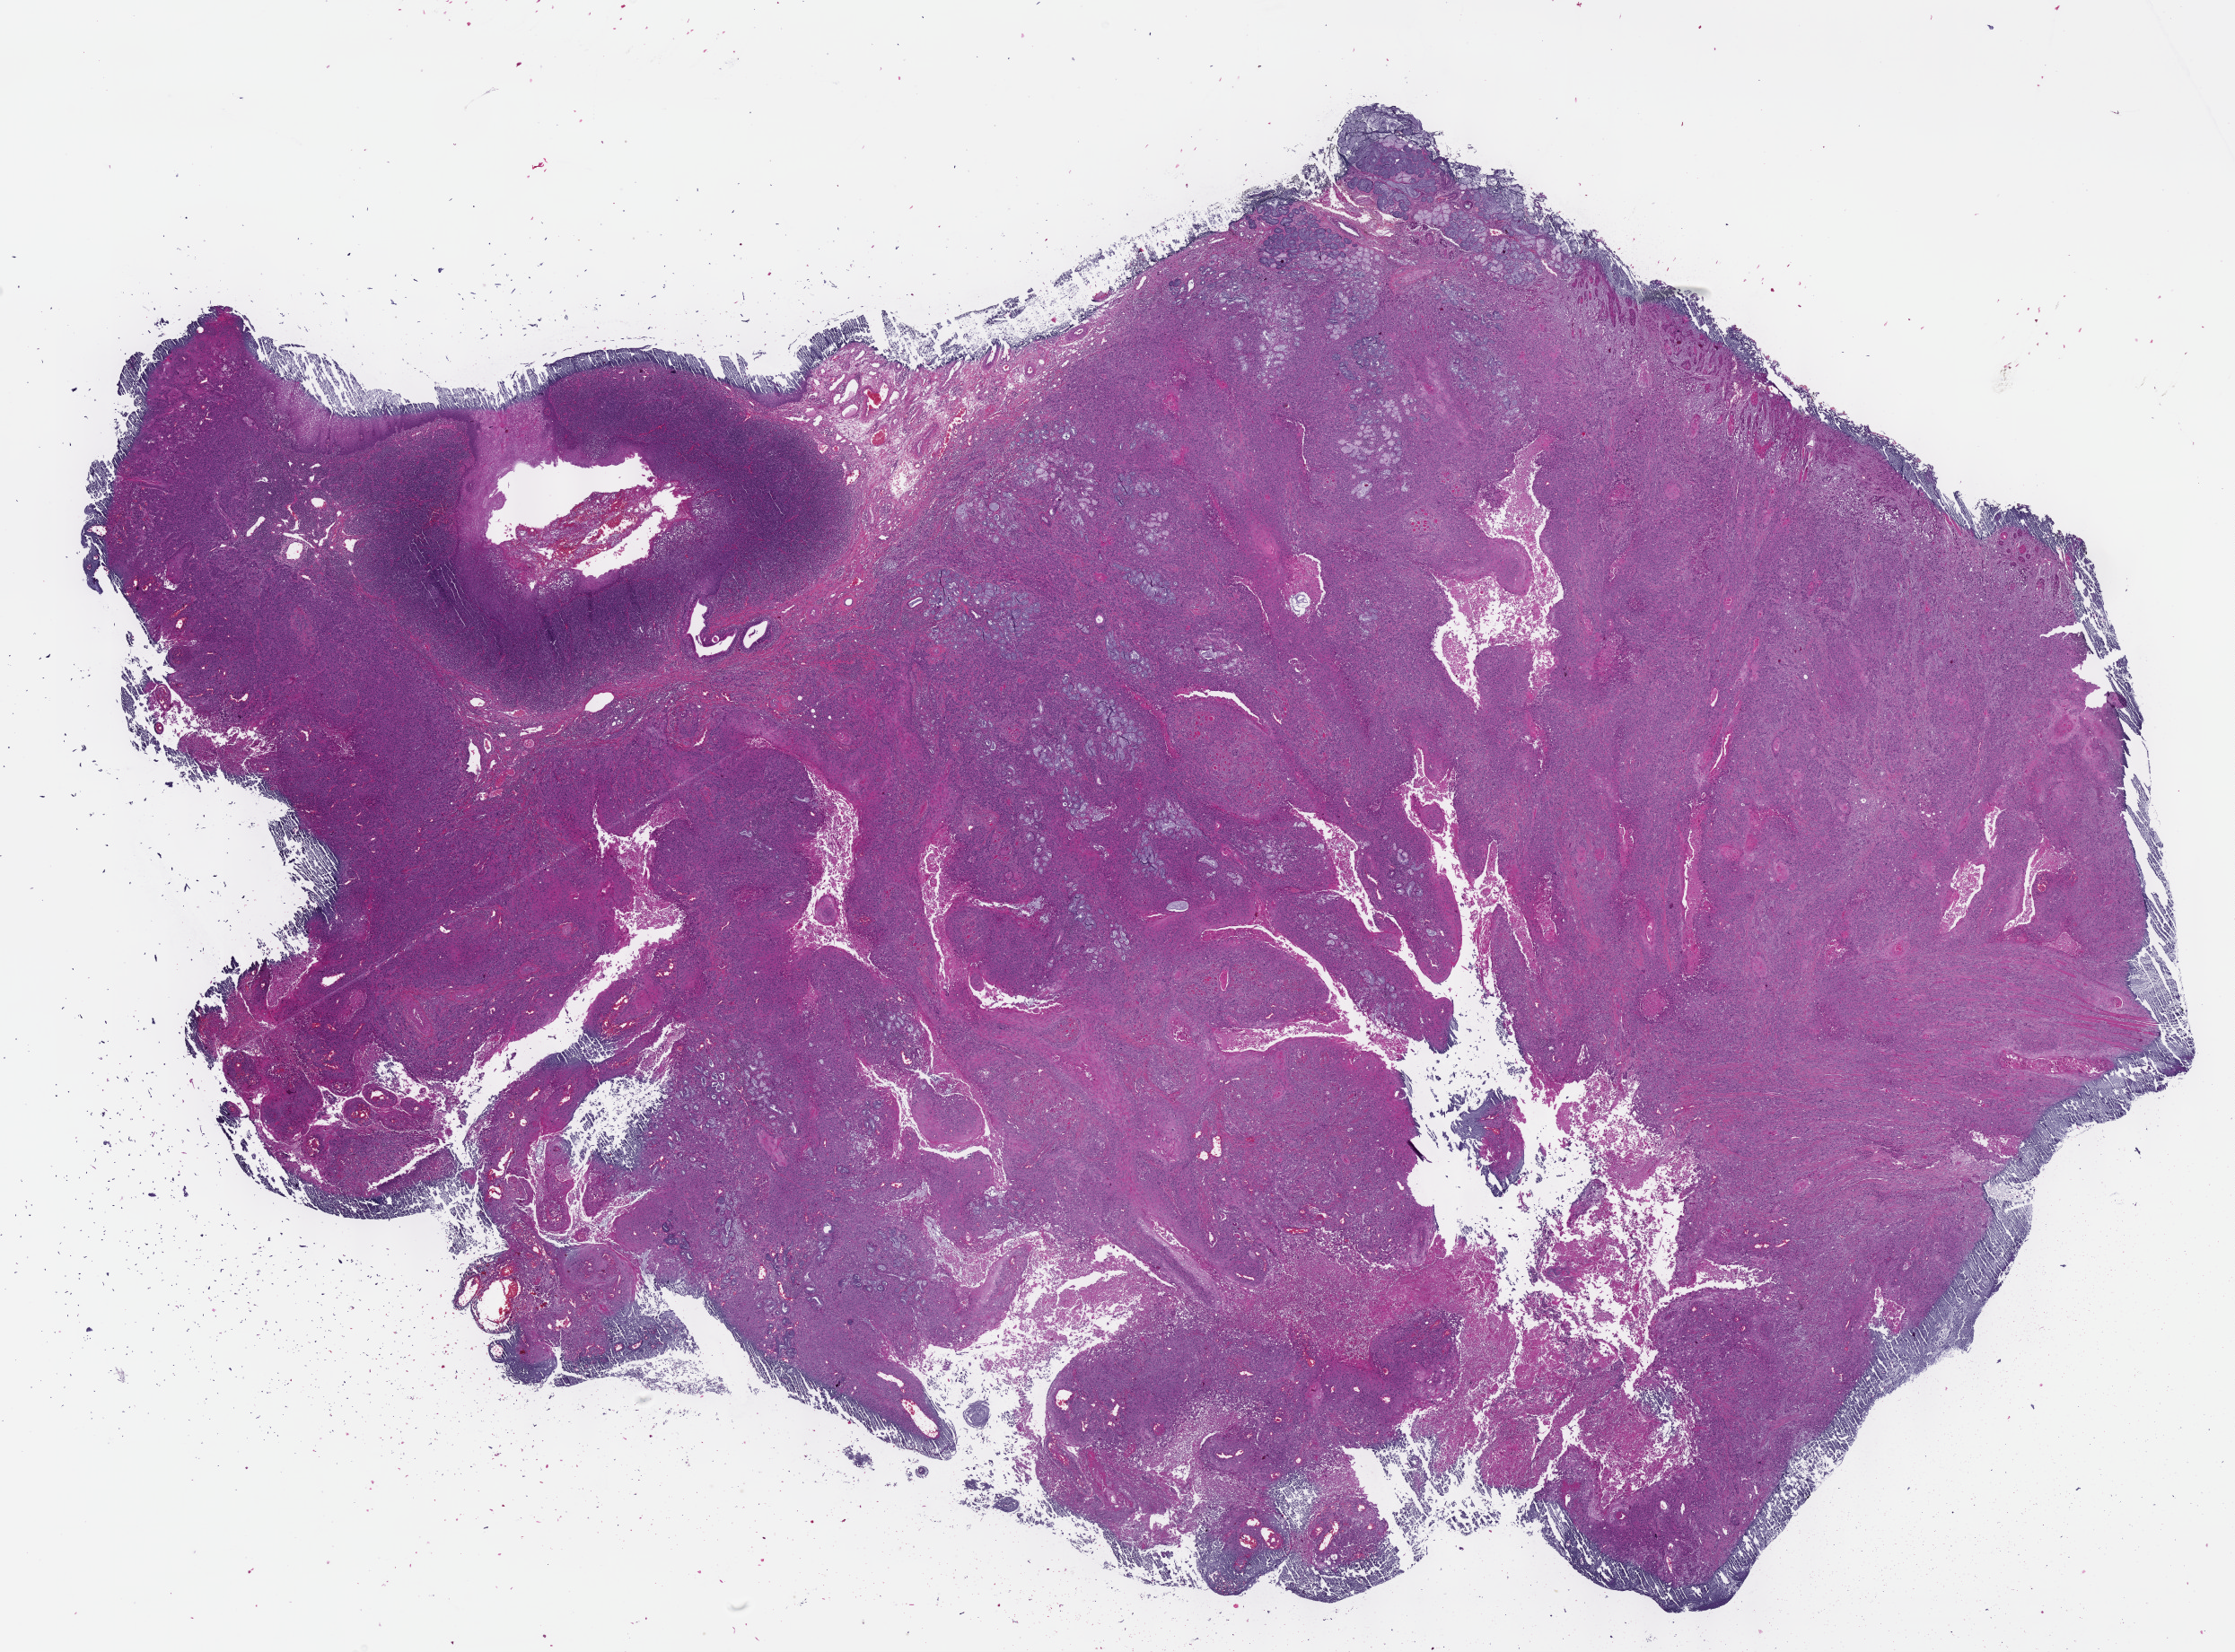
Whole-slide histology image, Hematoxylin and eosin (H&E) stained, whole scanned area (about 20.1 x 14.9 mm, slide scanned at 40x) shown as a low-resolution overview; formalin-fixed paraffin-embedded (FFPE) diagnostic section; head and neck, primary tumour sample. Male patient; age at initial diagnosis 64 years.
Histologic diagnosis: Squamous cell carcinoma, NOS (base of tongue, NOS).